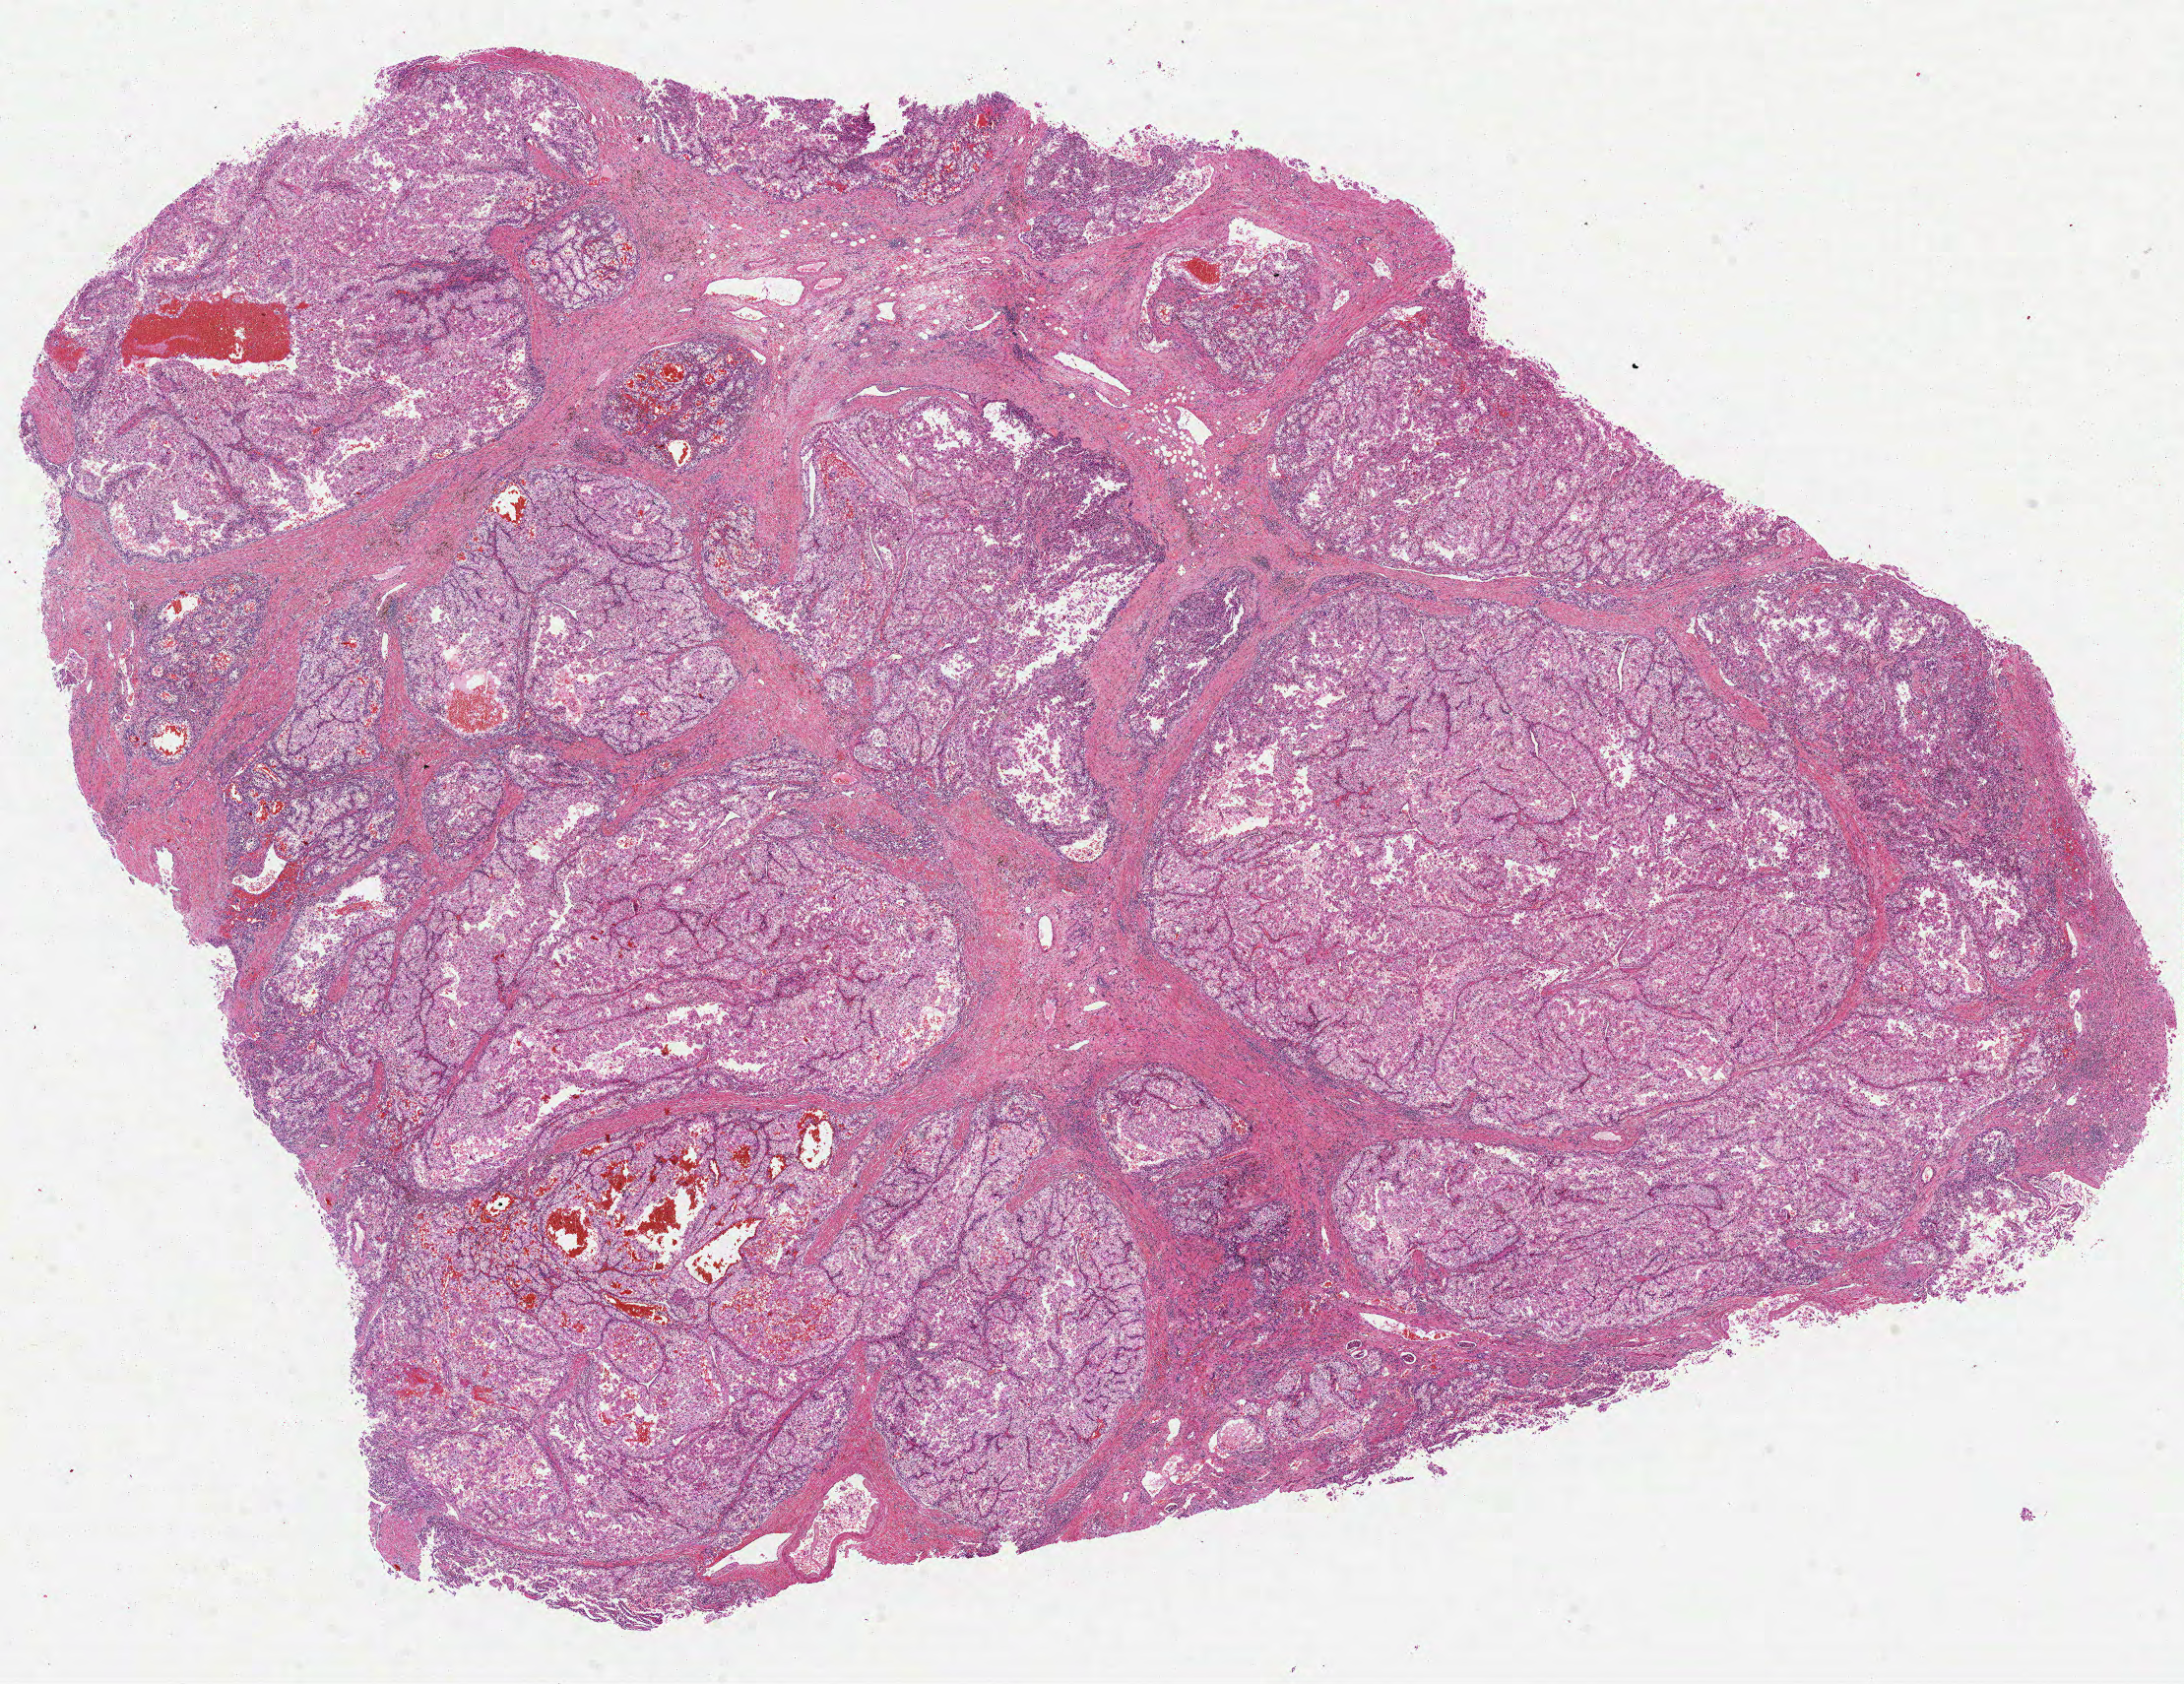
Digitized Hematoxylin and eosin (H&E) stained tissue section (whole slide) — whole scanned area (about 17.9 x 13.8 mm, from a 40x scan) shown as a low-resolution overview. Formalin-fixed paraffin-embedded (FFPE) diagnostic section. Primary tumour sample from the kidney. Male, age 52 years at initial diagnosis. Histologic grade: G2 (moderately differentiated).
* histologic diagnosis: Clear cell adenocarcinoma, NOS